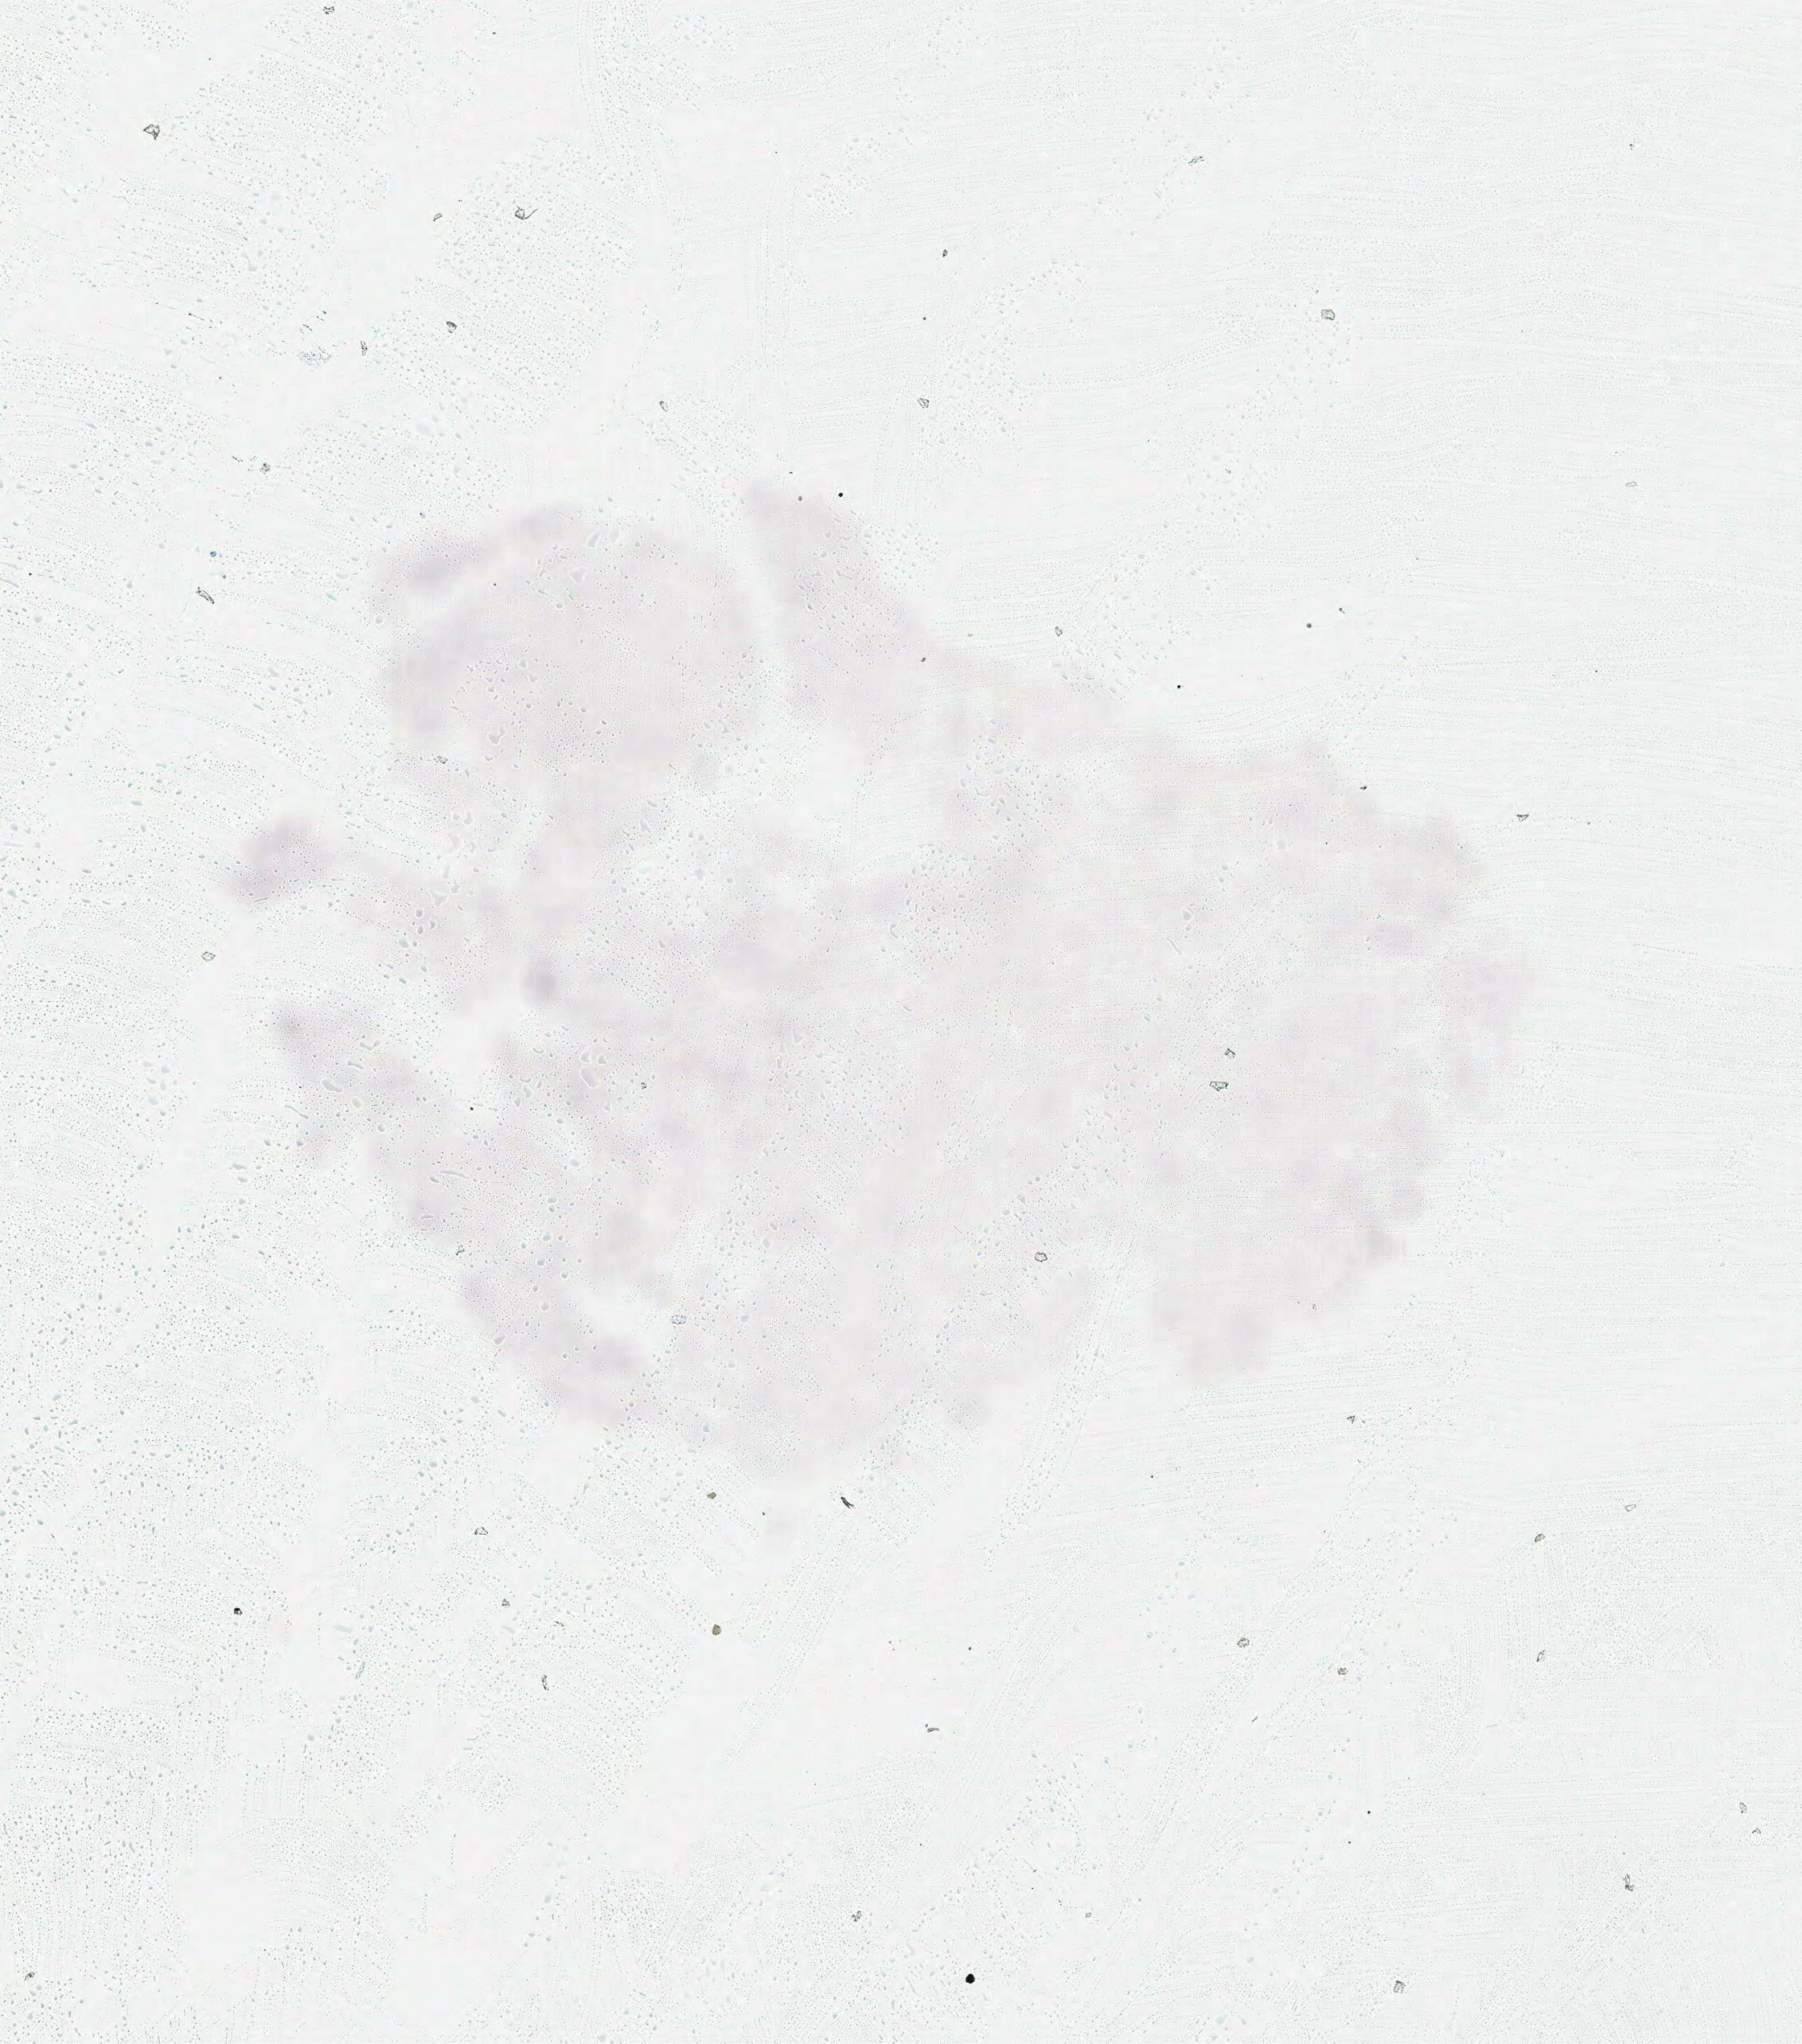
Whole-slide histology image, Hematoxylin and eosin (H&E) stained, shown as a low-resolution overview of the whole scanned area (about 4.4 x 5.0 mm); formalin-fixed paraffin-embedded (FFPE) diagnostic section; sample: primary tumour, brain. Male, age 58 years at initial diagnosis.
Diagnosis: Glioblastoma.